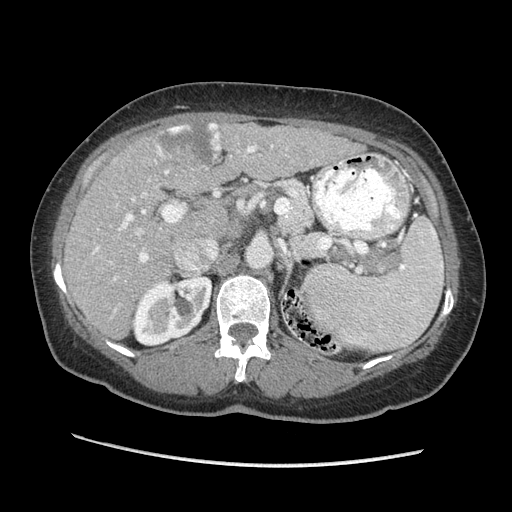
Contrast-enhanced abdominal CT (liver protocol), one axial slice; position 128 of 170 along the scan axis; reconstruction kernel STANDARD; 140 kVp; soft-tissue window (W 400 / L 40 HU); 2.5 mm slice thickness; 512 × 512 image matrix, field of view 360 × 360 mm. Case-level facts recorded for this patient, not image findings: diagnosis: hepatocellular carcinoma (patient treated with transarterial chemoembolisation; whether this scan precedes or follows treatment is not stated here); TNM stage (as recorded): Stage-II; Child-Pugh class: A; tumour nodularity: multinodular.
Structures marked on this image (semi-automatically segmented with operator editing):
- liver parenchyma outside the tumour (the mass and vessels are separate outlines, so this box may not span the whole liver): bounding box [x1, y1, x2, y2] px = [64, 122, 362, 338]
- mass: [156, 122, 221, 172]
- liver vessels: [92, 145, 287, 311]